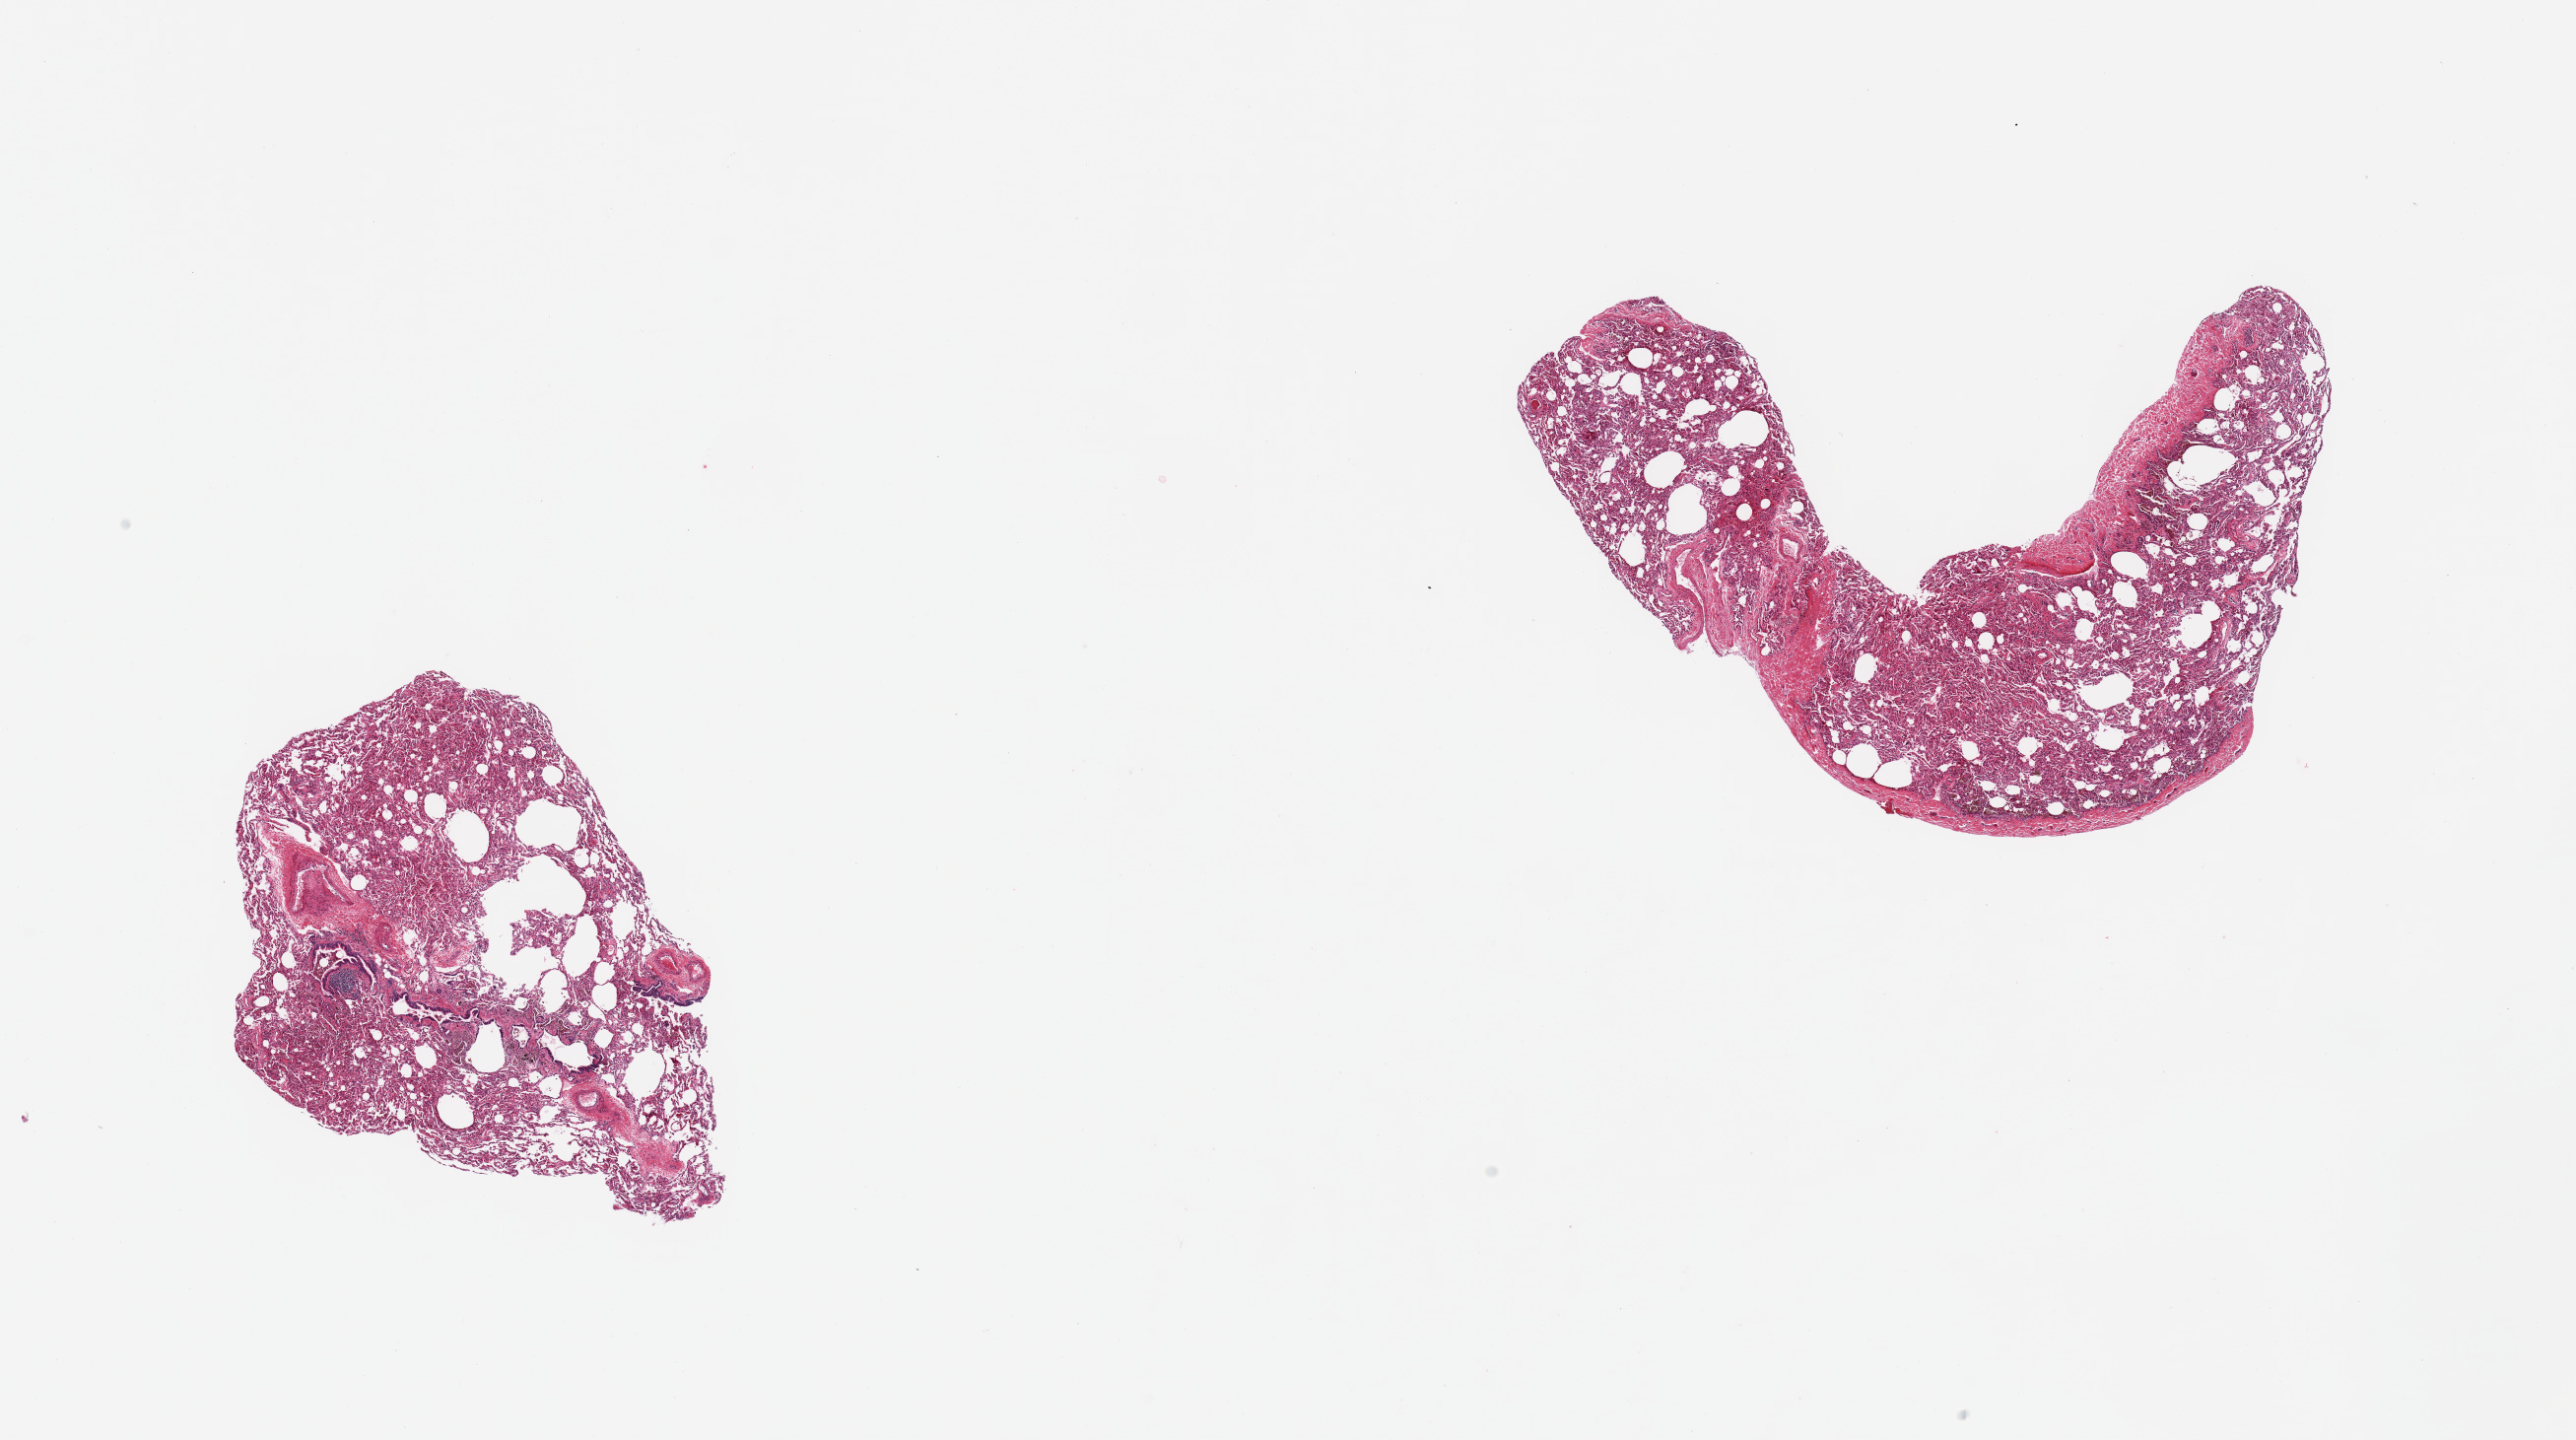
Digitized haematoxylin and eosin-stained section, brightfield — whole scanned area (about 20.7 x 11.6 mm) shown as a low-resolution overview; PAXgene-fixed, paraffin-embedded tissue; section of lung (target tissue); donor tissue sample. Donor: male.
* review note (as recorded): 2 pieces, trace edema, pronounced ataletctasis